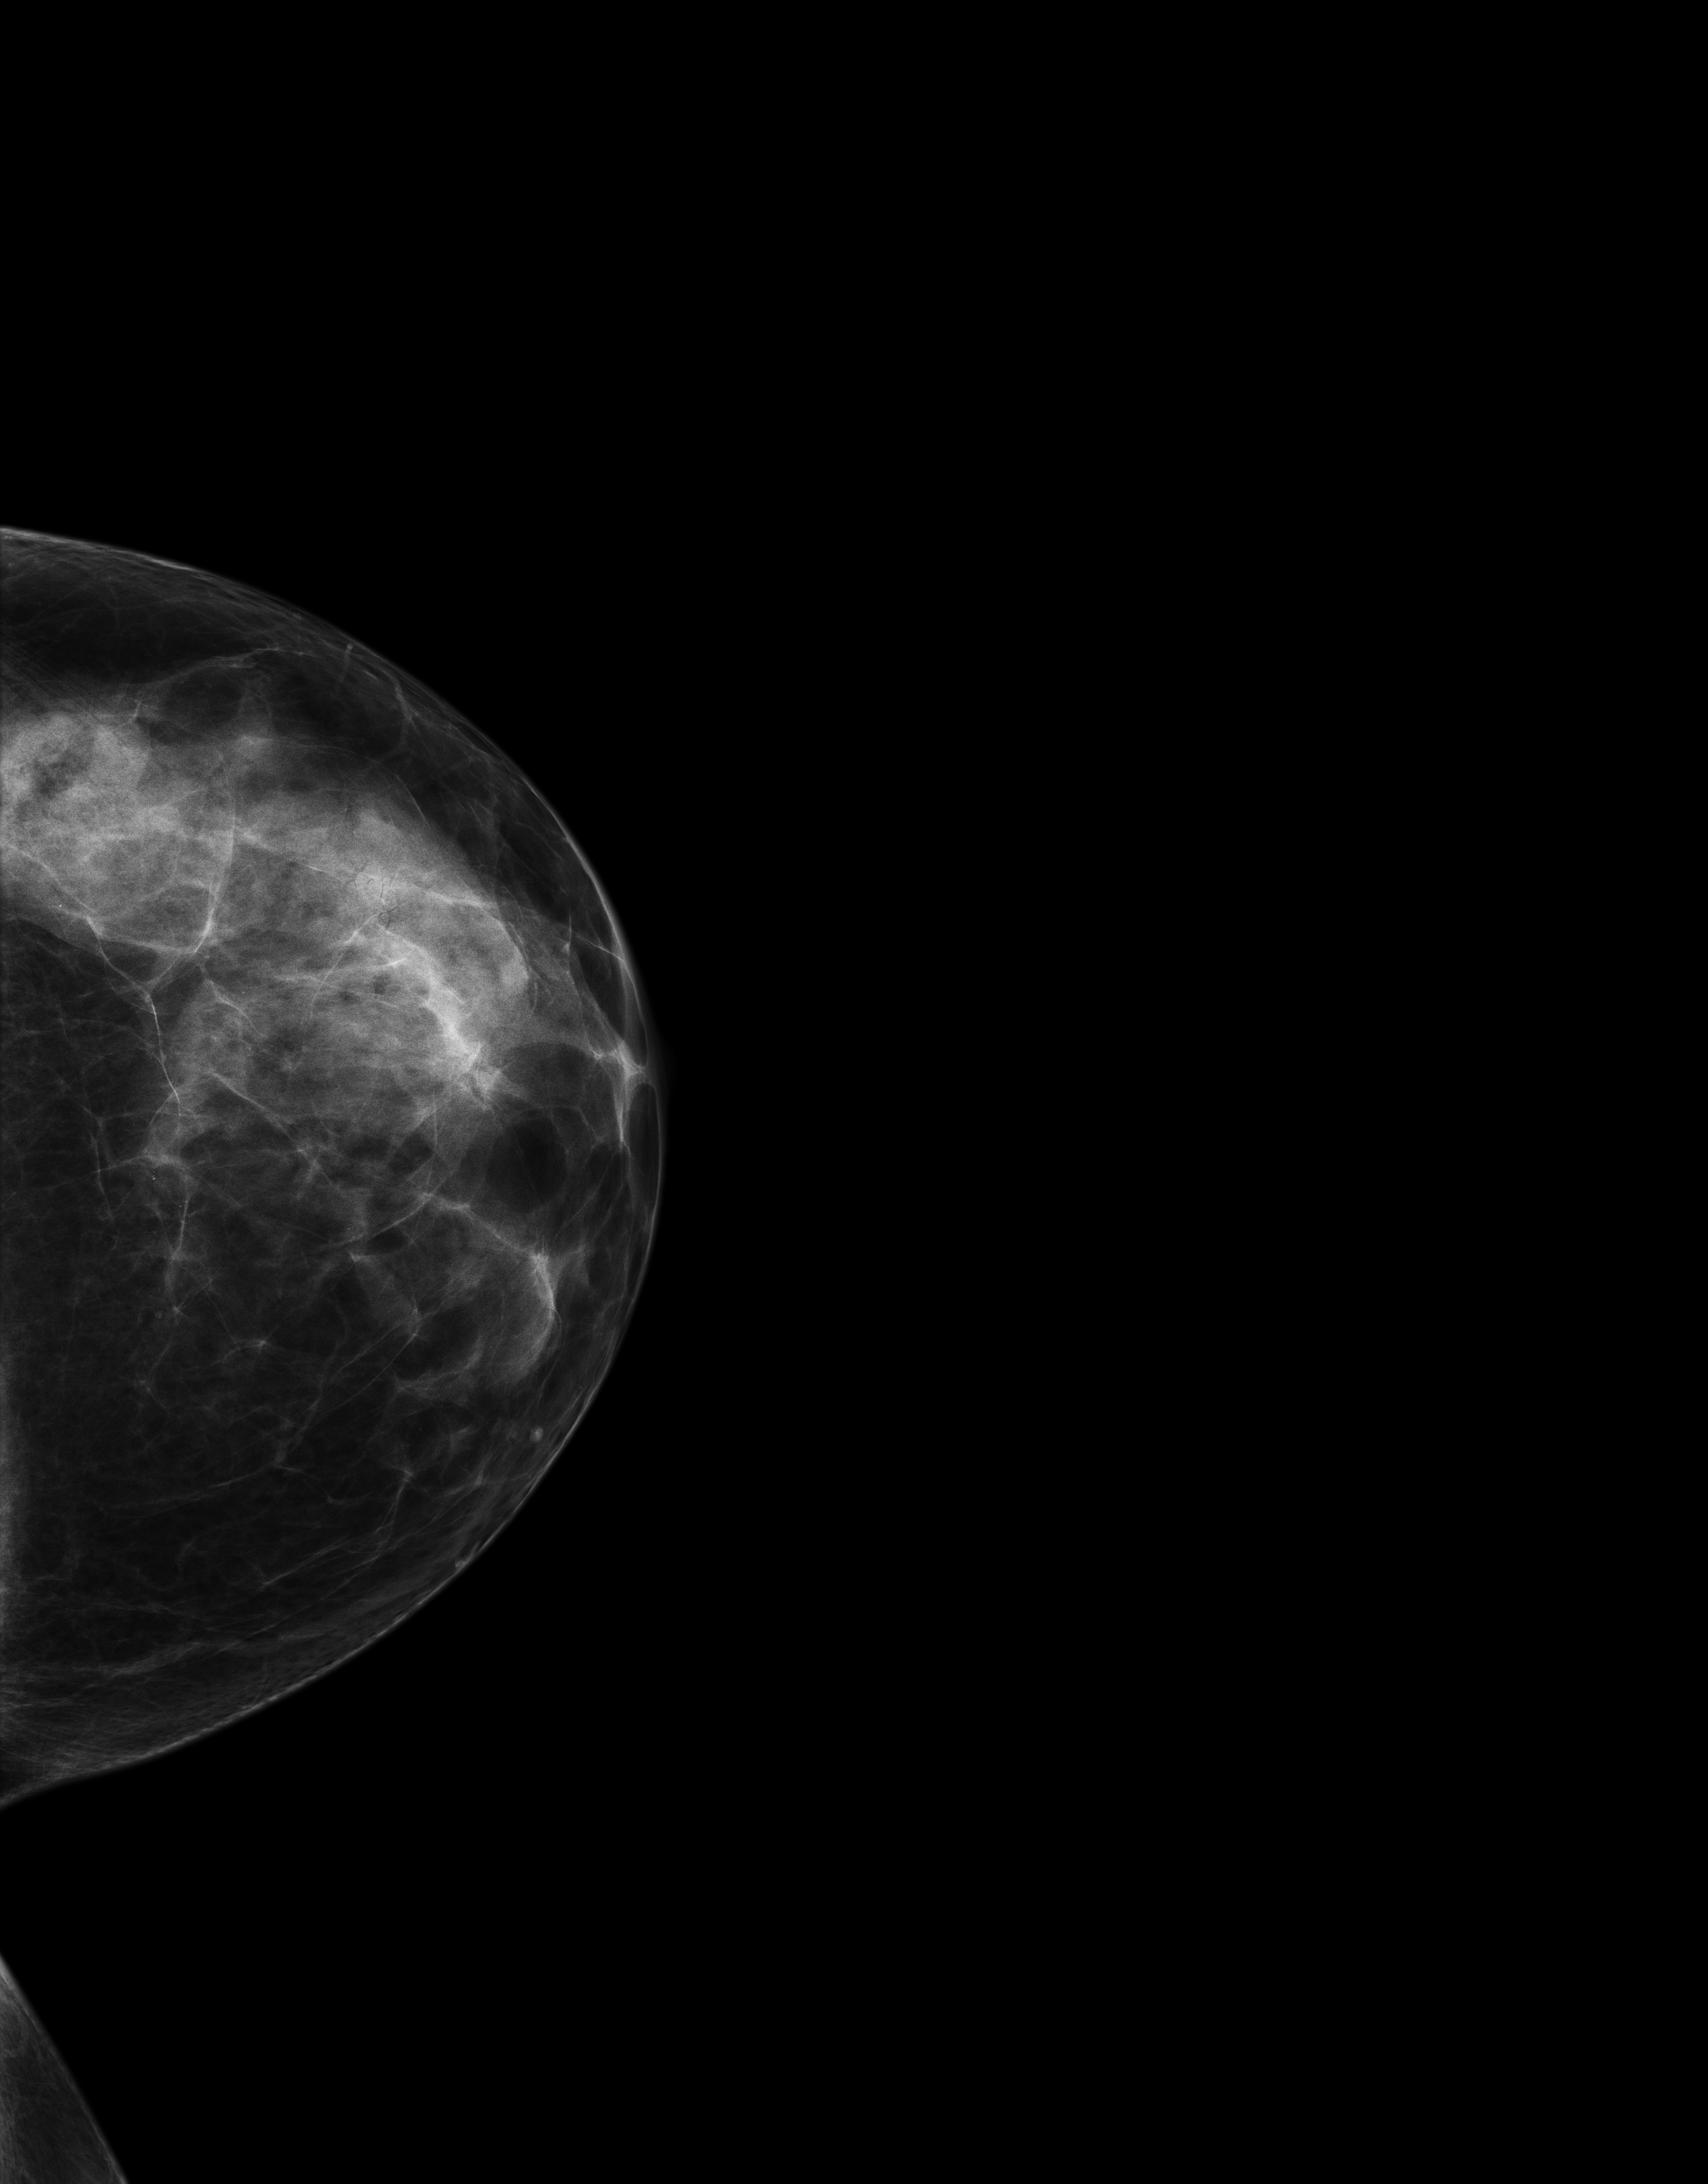
Full-field digital mammogram (FFDM); left breast; craniocaudal (CC) view; screening examination; compressed breast thickness 54 mm; system: Senographe Essential ADS_56.21.3. Female patient, age 51 years.
Breast density at the screening exam (both breasts): heterogeneously dense (BI-RADS density category c). Final BI-RADS assessment for this screening round (tomosynthesis exam, both breasts): category 1. Recall: no recall after this screen.